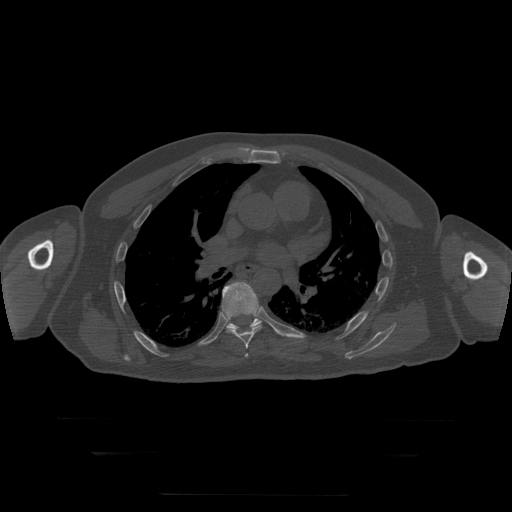
CT including the spine, one axial slice; slice 180 of 397 in the series (ordered by position); reconstruction kernel STANDARD; bone window (W 1800 / L 400 HU); 1.25 mm slice thickness; 512 × 512 image matrix, field of view 510 × 510 mm. Patient age 73 years. From the clinical record (not read from this slice): primary cancer: prostate.
Structures marked on this image (semi-automatically segmented with operator editing):
- T6 vertebra: bounding box (x1, y1, x2, y2) in pixels: (245, 354, 249, 358)
- T7 vertebra: (222, 282, 262, 349)
- T8 vertebra: (227, 319, 287, 337)